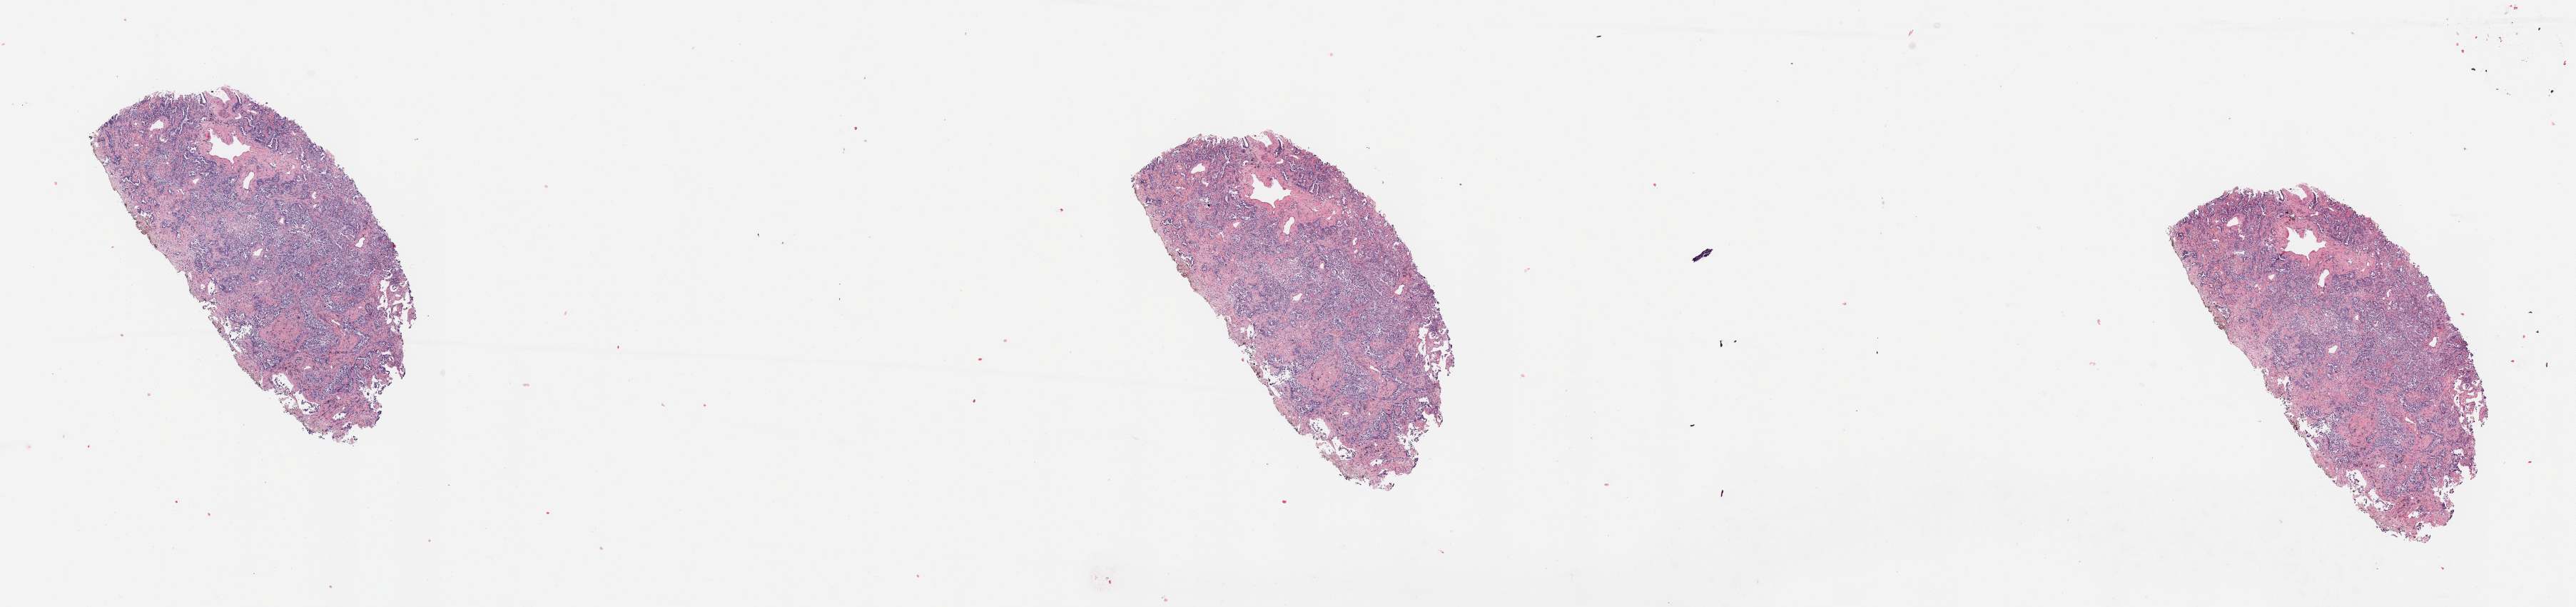
H&E whole-slide image, a low-resolution overview of the entire scanned area, about 28.5 x 6.7 mm; tumour tissue sample, sampled site: lung. 68-year-old female patient. Composition of this section per pathologist review: tumour nuclei 75%, necrosis 5%.
Histologic diagnosis: Adenocarcinoma, NOS.